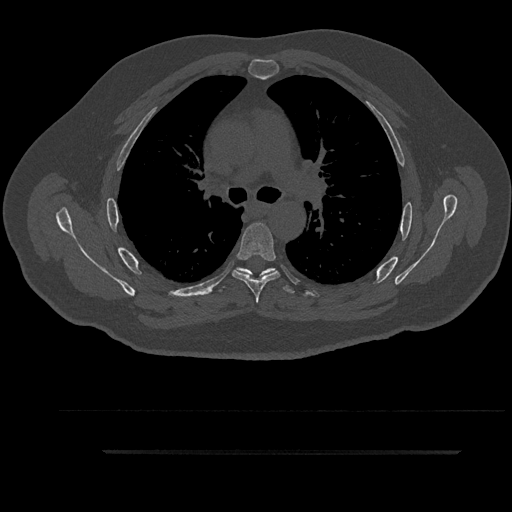
CT including the spine, one axial slice. Position 618 of 797 along the scan axis. Reconstruction kernel Br40s/3. Bone window (W 1800 / L 400 HU). 0.5 mm slice thickness. 512 × 512 image matrix, field of view 432 × 432 mm. Patient: male, 63 years. From the clinical record (not read from this slice): primary cancer: renal.
Structures marked on this image (semi-automatic segmentation, software-assisted and operator-edited):
- T5 vertebra: bounding box (x1, y1, x2, y2) in pixels: (232, 223, 280, 303)
- T6 vertebra: (219, 268, 295, 294)